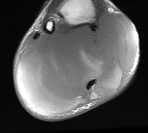
MRI of an extremity soft-tissue mass, one axial slice; position 21 of 76 along the scan axis; MR volume resampled by the dataset authors to the PET/CT grid (not the native acquisition matrix); 3.27 mm slice thickness; 148 × 133 image matrix, field of view 145 × 130 mm. Male patient. From the clinical record (not read from this slice): histological type: liposarcoma - round cell; grade: high; site of the primary tumour: right calf.
Annotated regions visible in this slice (expert contour drawn on MRI and transferred to this co-registered scan by the dataset authors):
- gross tumour volume (mass): bounding box <15,14,137,113> (left, top, right, bottom; pixels)